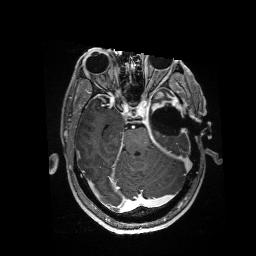
Brain MRI from a brain-tumour surgery series, one axial slice; position 107 of 176 along the scan axis; T1-weighted post-contrast; 256 × 256 image matrix, field of view 256 × 256 mm. Case-level facts recorded for this patient, not image findings: histopathology: Glioblastoma; WHO grade: 4; IDH mutation: no.
Outlined on this slice (outlined manually by an expert reader):
- residual tumour: bounding box (x1, y1, x2, y2) in pixels: (152, 92, 184, 117)